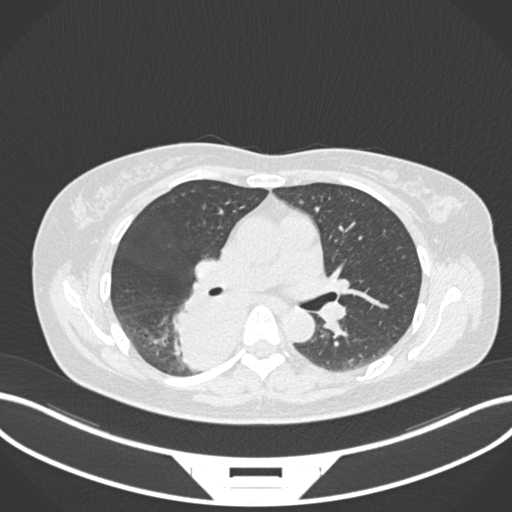
Chest CT, one axial slice. Slice 603 of 677 in the series (ordered by position). Lung window (W 1500 / L -600 HU). 1 mm slice thickness. 512 × 512 image matrix, field of view 400 × 400 mm. Female patient, age 54 years. From the clinical record (not read from this slice): clinical TNM (as recorded): T4 N0 M0.
Structures marked on this image (bounding box drawn by a radiologist):
- lung tumour (recorded histology: adenocarcinoma): bounding box <172,285,250,373> (left, top, right, bottom; pixels)